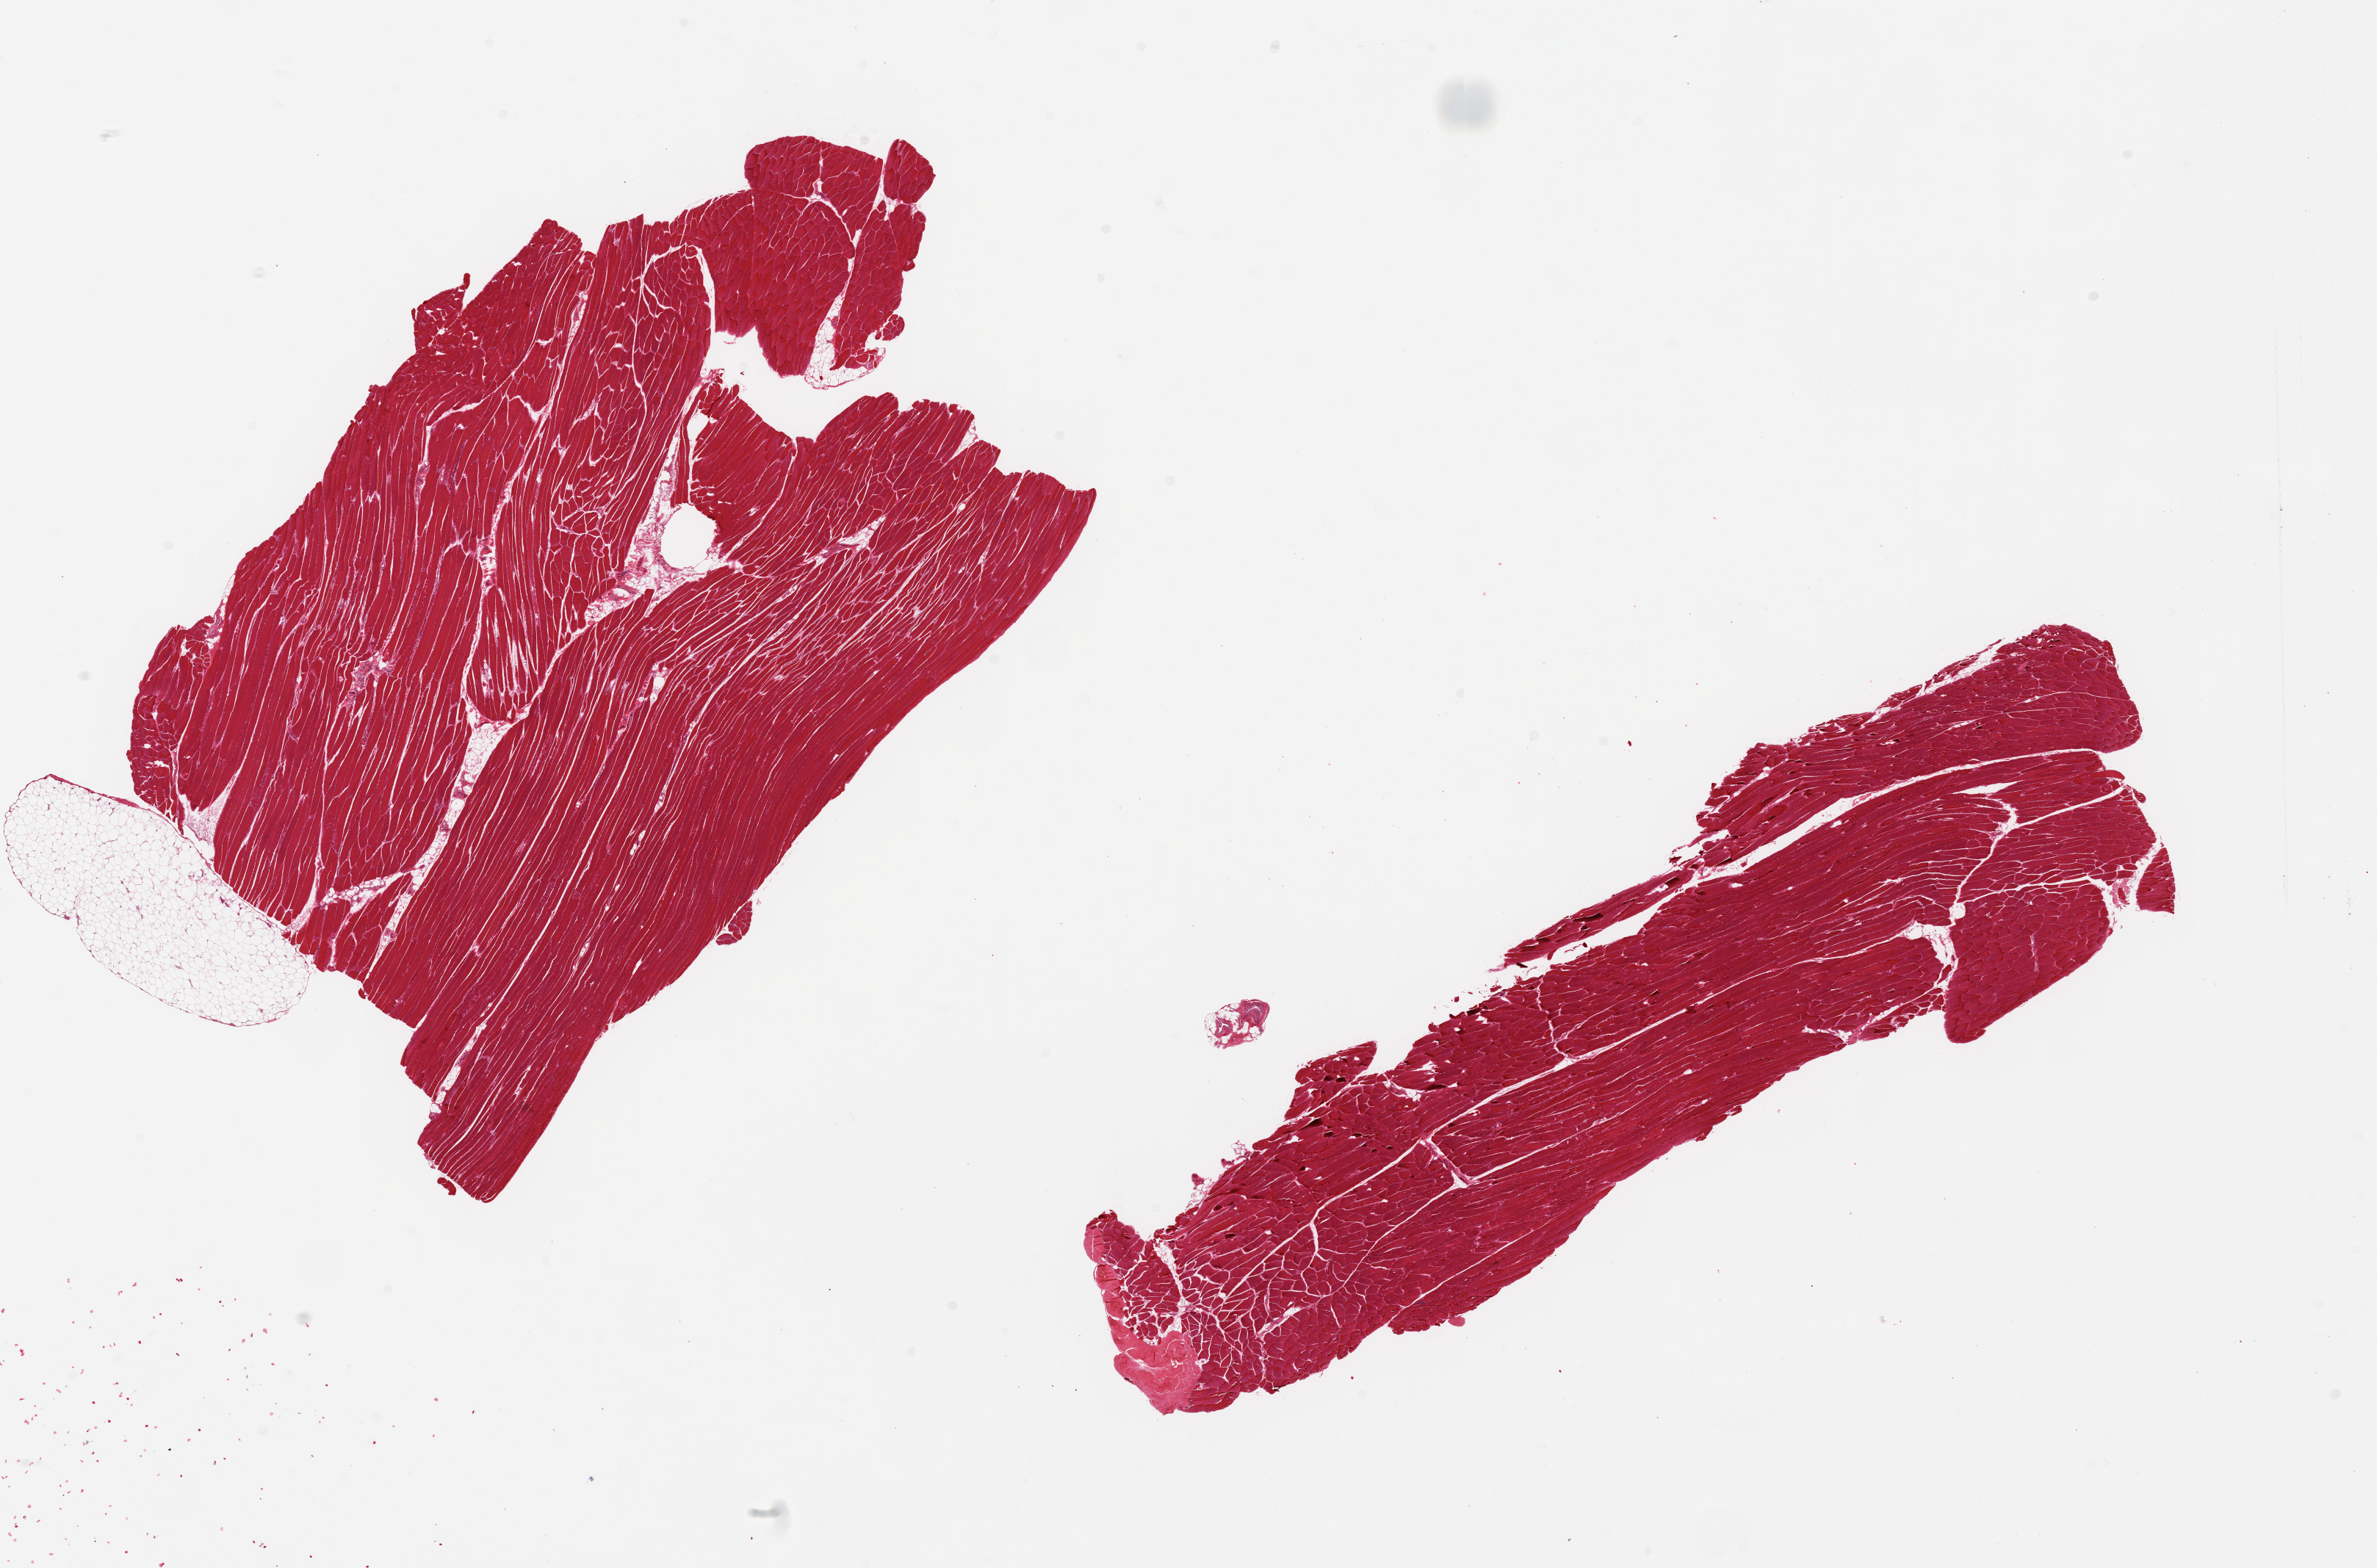
Digitized hematoxylin and eosin (H&E)-stained section — low-resolution overview of the scanned area, about 25.6 x 16.9 mm. PAXgene-fixed, paraffin-embedded tissue. Sampled site (target tissue): skeletal muscle. Tissue donor sample.
Pathologist's review note for this sample: 2 pieces; small attached portions of fat and tendon.